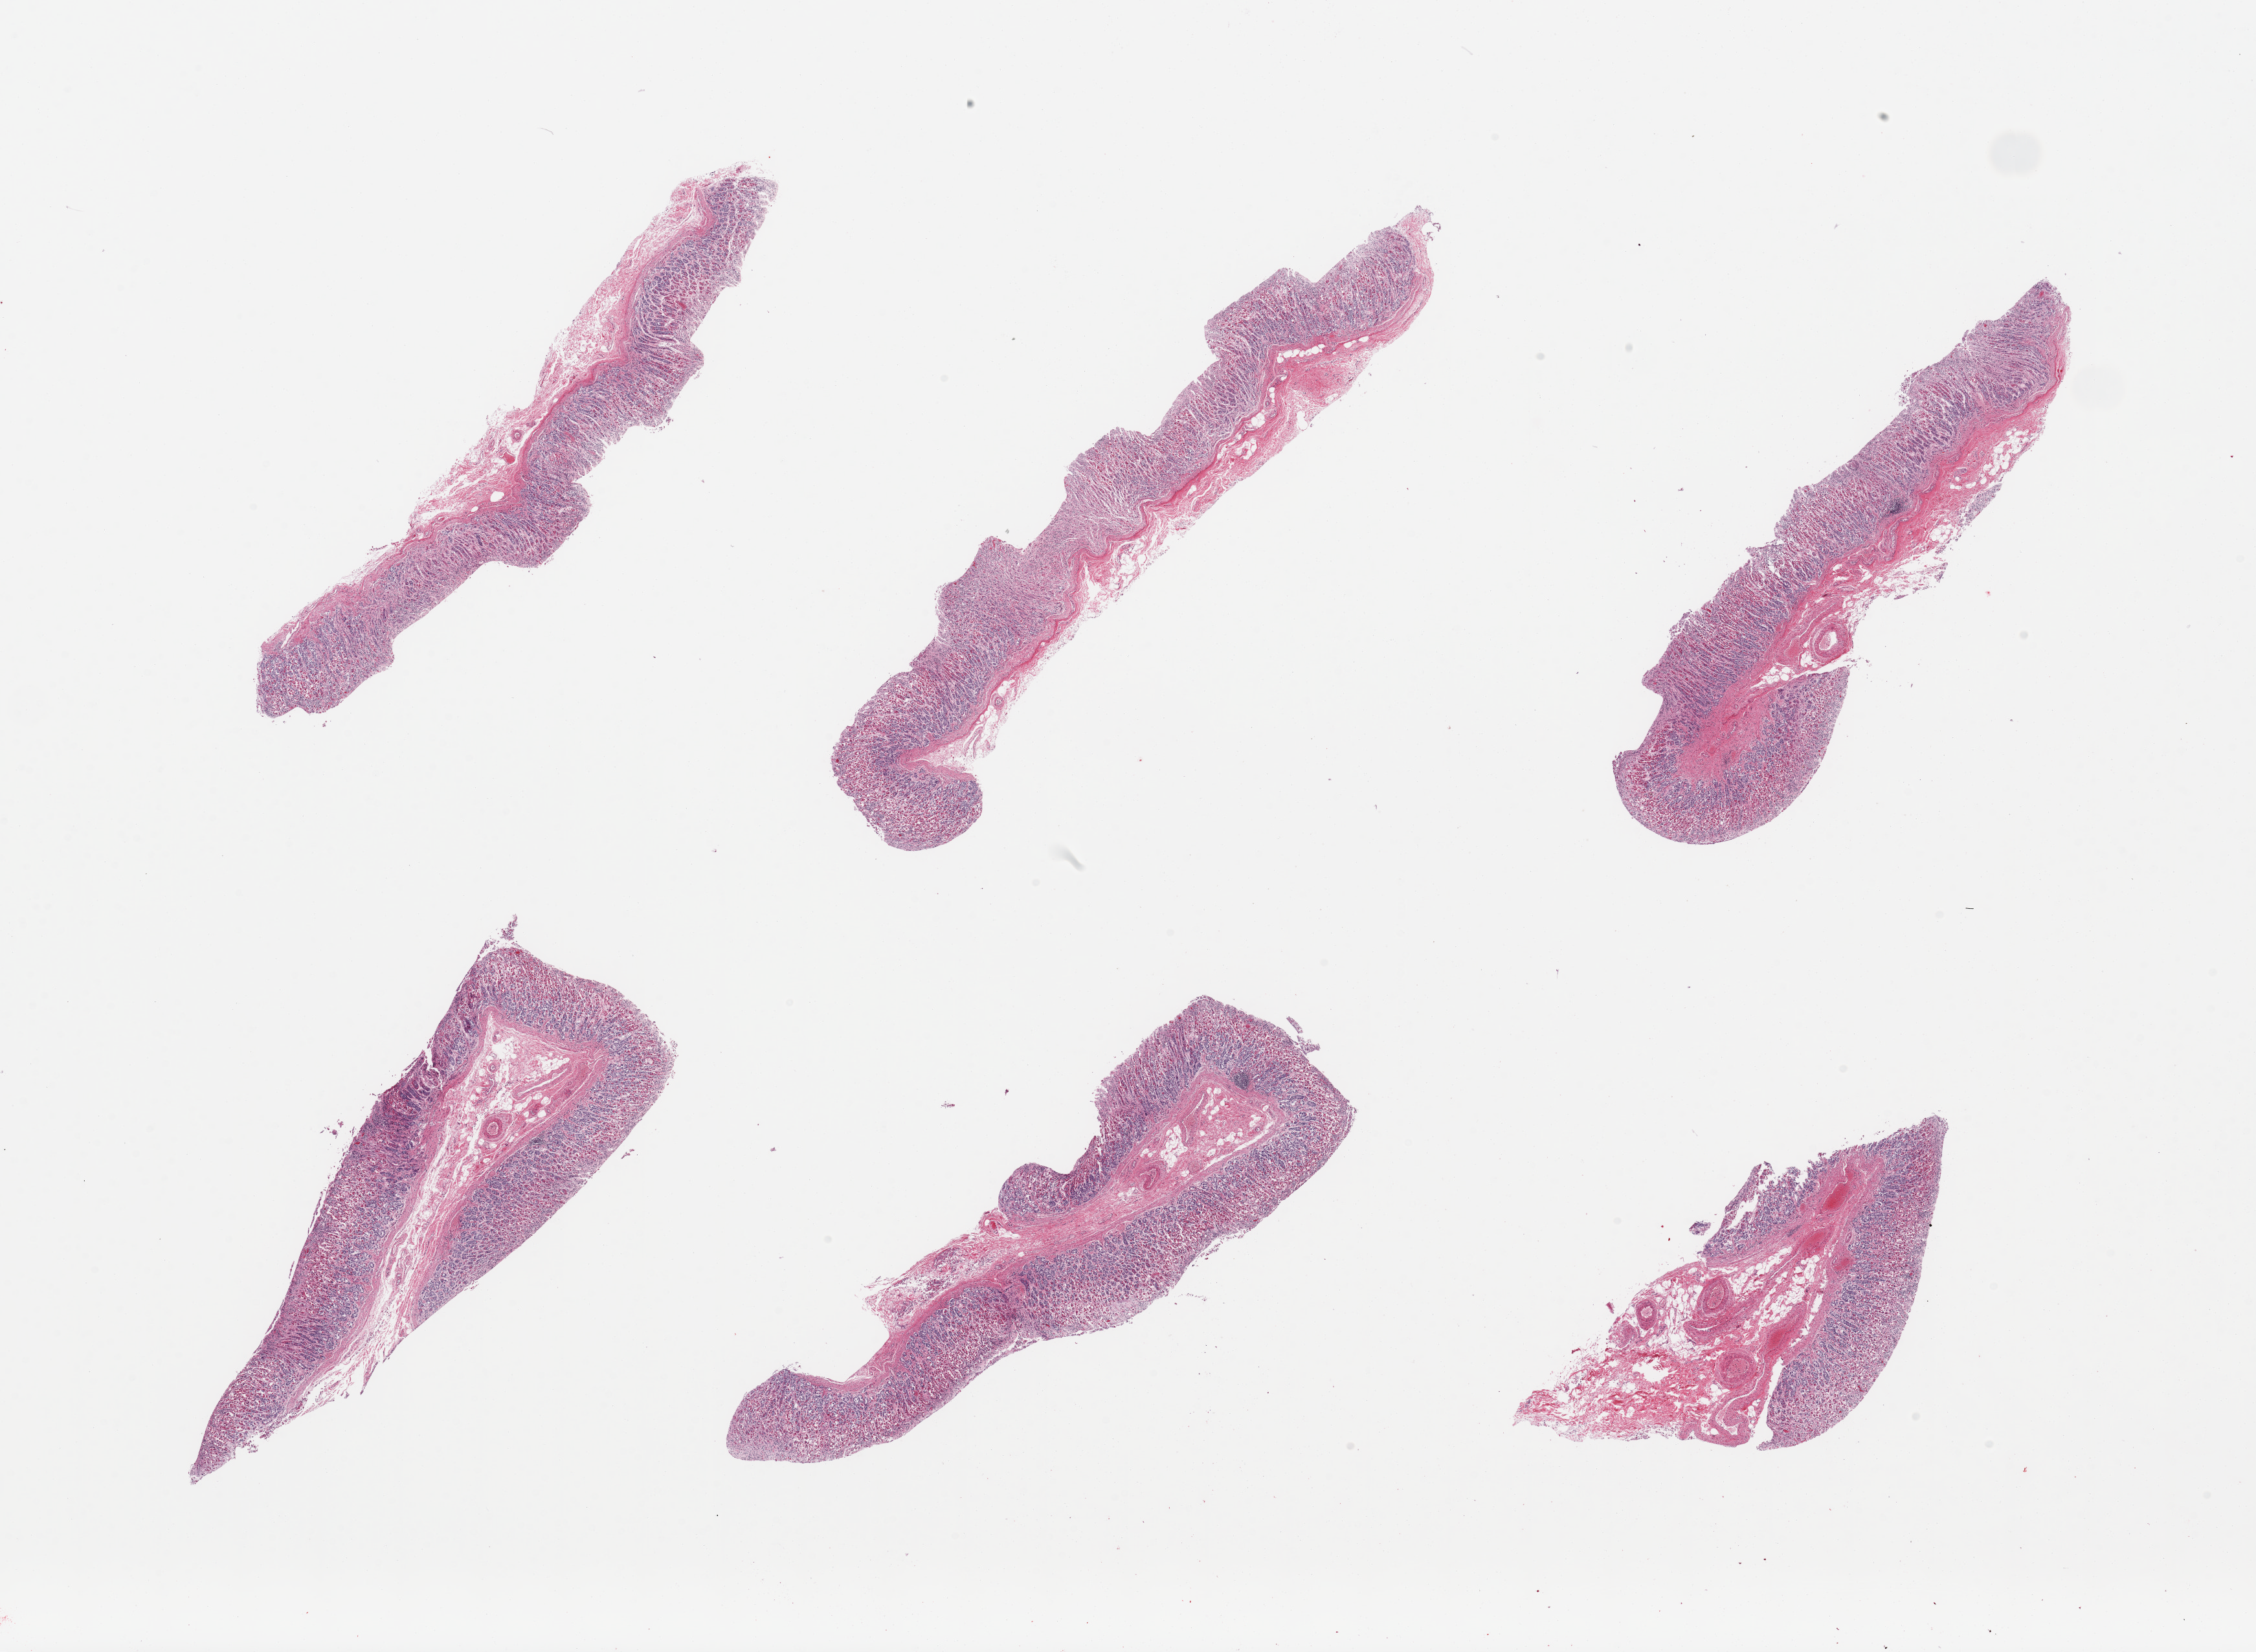
Haematoxylin and eosin whole-slide image, brightfield — a low-resolution overview of the entire scanned area, about 27.6 x 20.2 mm; PAXgene-fixed paraffin-embedded (PFPE) section; section of stomach (target tissue); donor tissue sample. Donor sex: male.
Reviewer comment on this tissue sample: 6 pieces; autolyzed mucosa only, no muscularis.